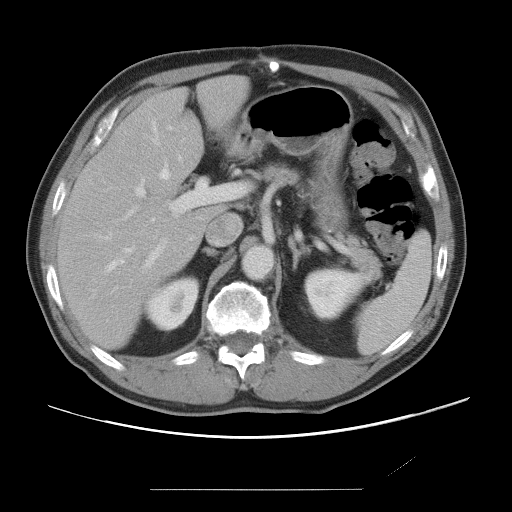
Contrast-enhanced abdominal CT, one axial slice. Slice 44 of 87 in the series (ordered by position). 120 kVp. Intravenous contrast given. Soft-tissue window (W 400 / L 40 HU). 5 mm slice thickness. 512 × 512 image matrix, field of view 406 × 406 mm. Male patient, age 74 years. From the clinical record (not read from this slice): diagnosis: colorectal cancer liver metastases, imaged before liver resection; multiple liver metastases: yes; largest metastasis: 1.1 cm; chemotherapy before resection: yes.
Structures marked on this image (manually delineated by an expert):
- hepatic veins: bounding box [x1, y1, x2, y2] px = [106, 124, 182, 269]
- liver: [59, 76, 249, 348]
- planned liver remnant (the part of the liver to remain after resection): [59, 76, 249, 348]
- portal vein (with intrahepatic branches): [127, 179, 247, 267]